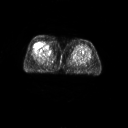
FDG PET of an extremity soft-tissue mass (from a PET/CT study), one axial slice. Position 17 of 267 along the scan axis. 3.27 mm slice thickness. 128 × 128 image matrix. Female patient, age 56 years. From the clinical record (not read from this slice): histological type: malignant solitary fibrous tumor; grade: intermediate; site of the primary tumour: right thigh.
Annotated regions visible in this slice (expert contour drawn on MRI and transferred to this co-registered scan by the dataset authors):
- gross tumour volume including surrounding oedema: bounding box (x1, y1, x2, y2) in pixels: (40, 41, 51, 49)